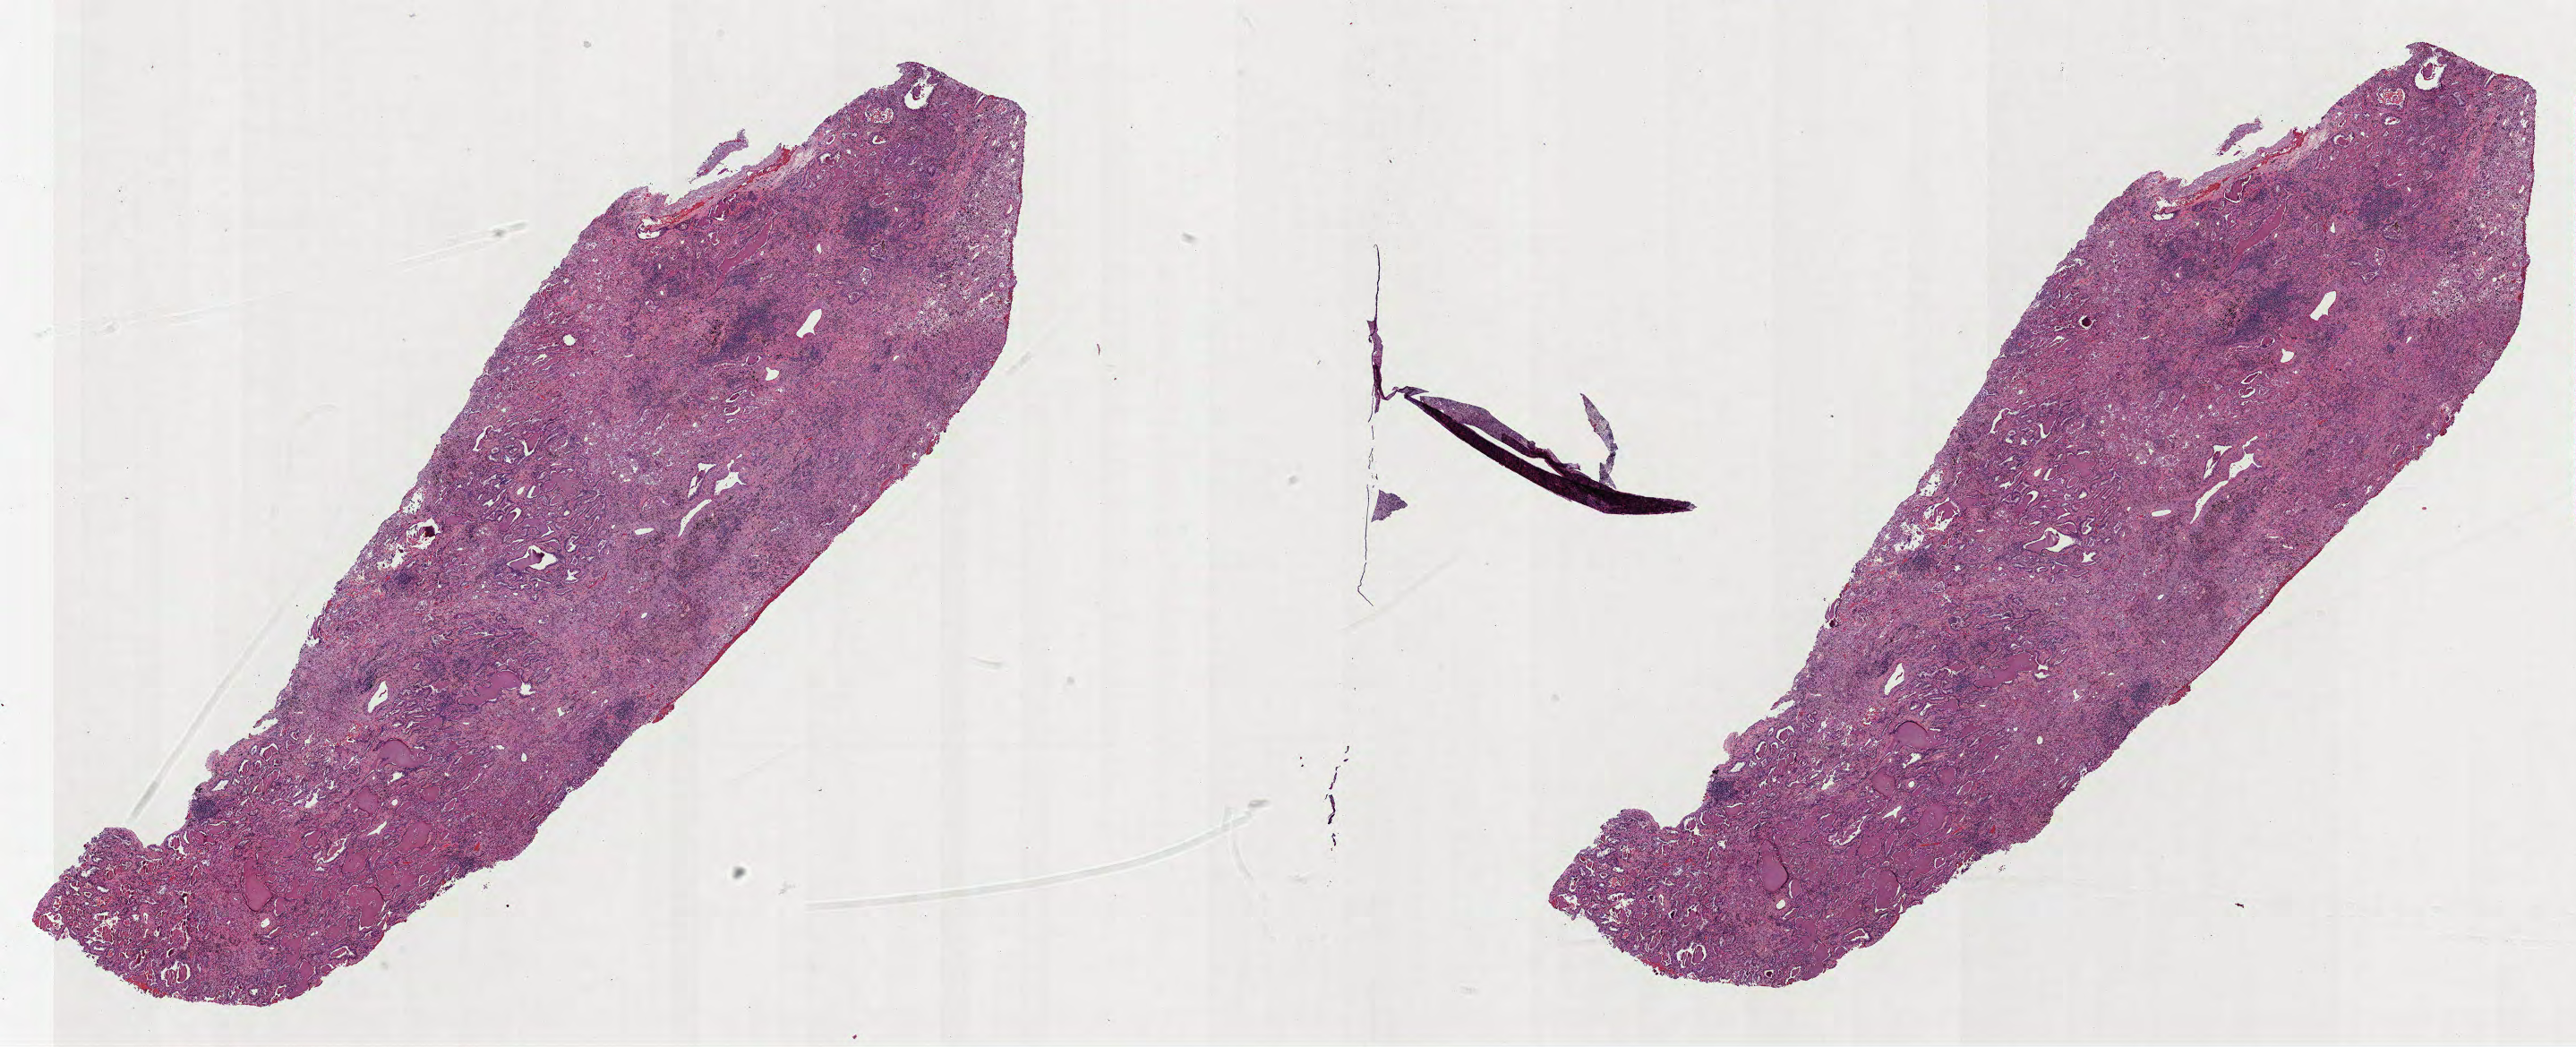
Hematoxylin and eosin (H&E) stained whole-slide image, whole scanned area (about 23.2 x 9.4 mm, acquisition: 40x scan) shown as a low-resolution overview. Formalin-fixed paraffin-embedded (FFPE) diagnostic section. Lung, primary tumour sample. Patient: male, age at initial diagnosis 70 years.
Laterality: left. AJCC pathologic stage: IA (7th edition). Pathologic diagnosis: Adenocarcinoma, NOS (upper lobe, lung).